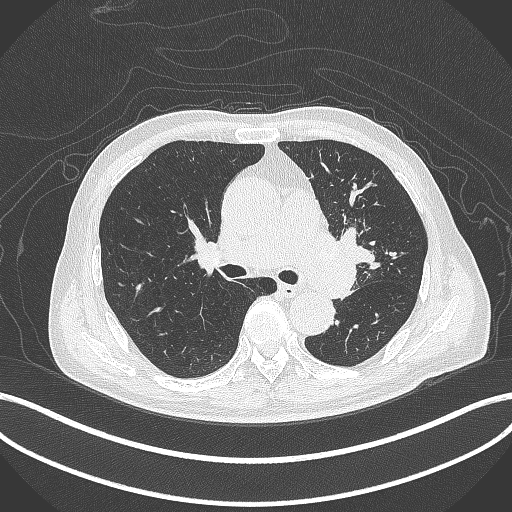
Chest CT, one axial slice; position 263 of 417 along the scan axis; reconstruction kernel B70f; 120 kVp; lung window (W 1500 / L -600 HU); 512 × 512 image matrix, field of view 400 × 400 mm. Male patient, age 77 years. From the clinical record (not read from this slice): clinical TNM (as recorded): T3 N1 M0.
Structures marked on this image (rectangle marked by the reading radiologist):
- lung tumour (recorded histology: adenocarcinoma): bounding box [x1, y1, x2, y2] px = [314, 229, 363, 302]